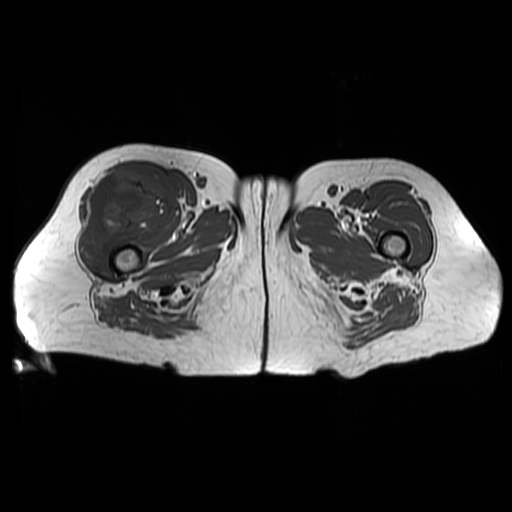
MRI of an extremity soft-tissue mass, one axial slice. Slice 35 of 48 in the series (ordered by position). 6 mm slice thickness. 512 × 512 image matrix. Female patient. From the clinical record (not read from this slice): histological type: pleiomorphic undifferentiated sarcoma; grade: high; site of the primary tumour: right quadricep.
Structures marked on this image (outlined manually by an expert reader):
- gross tumour volume including surrounding oedema: bounding box (x1, y1, x2, y2) in pixels: (79, 167, 171, 261)
- gross tumour volume (mass): (79, 167, 171, 261)